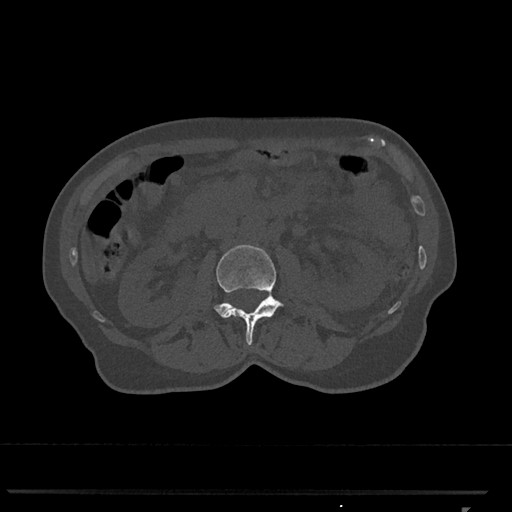
CT including the spine, one axial slice; slice 334 of 793 in the series (ordered by position); 120 kVp; bone window (W 1800 / L 400 HU); 0.5 mm slice thickness; 512 × 512 image matrix, field of view 380 × 380 mm. Patient: female, 62 years. Case-level facts recorded for this patient, not image findings: primary cancer: renal.
Annotated regions visible in this slice (semi-automatically segmented with operator editing):
- L2 vertebra: box from (x=214, y=245) to (x=284, y=345) px